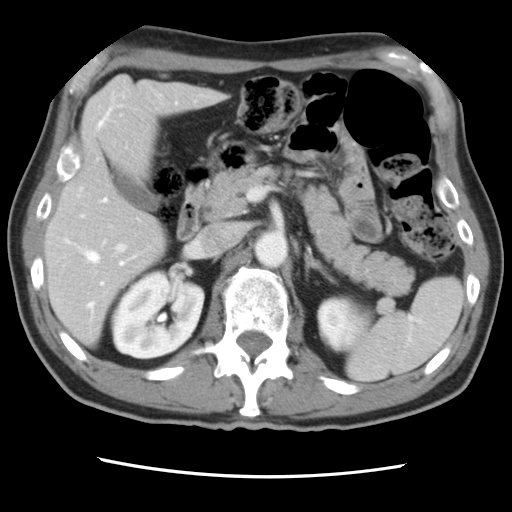
Contrast-enhanced abdominal CT, one axial slice. Slice 44 of 83 in the series (ordered by position). Intravenous contrast given. Soft-tissue window (W 400 / L 40 HU). 5 mm slice thickness. 512 × 512 image matrix, field of view 321 × 321 mm. Male patient, age 69 years. From the clinical record (not read from this slice): diagnosis: colorectal cancer liver metastases, imaged before liver resection; multiple liver metastases: yes; largest metastasis: 3.5 cm; chemotherapy before resection: yes.
Outlined on this slice (manually delineated by an expert):
- hepatic veins: bounding box <66,103,177,309> (left, top, right, bottom; pixels)
- liver: <47,78,222,344>
- planned liver remnant (the part of the liver to remain after resection): <46,147,168,344>
- portal vein (with intrahepatic branches): <77,187,127,253>